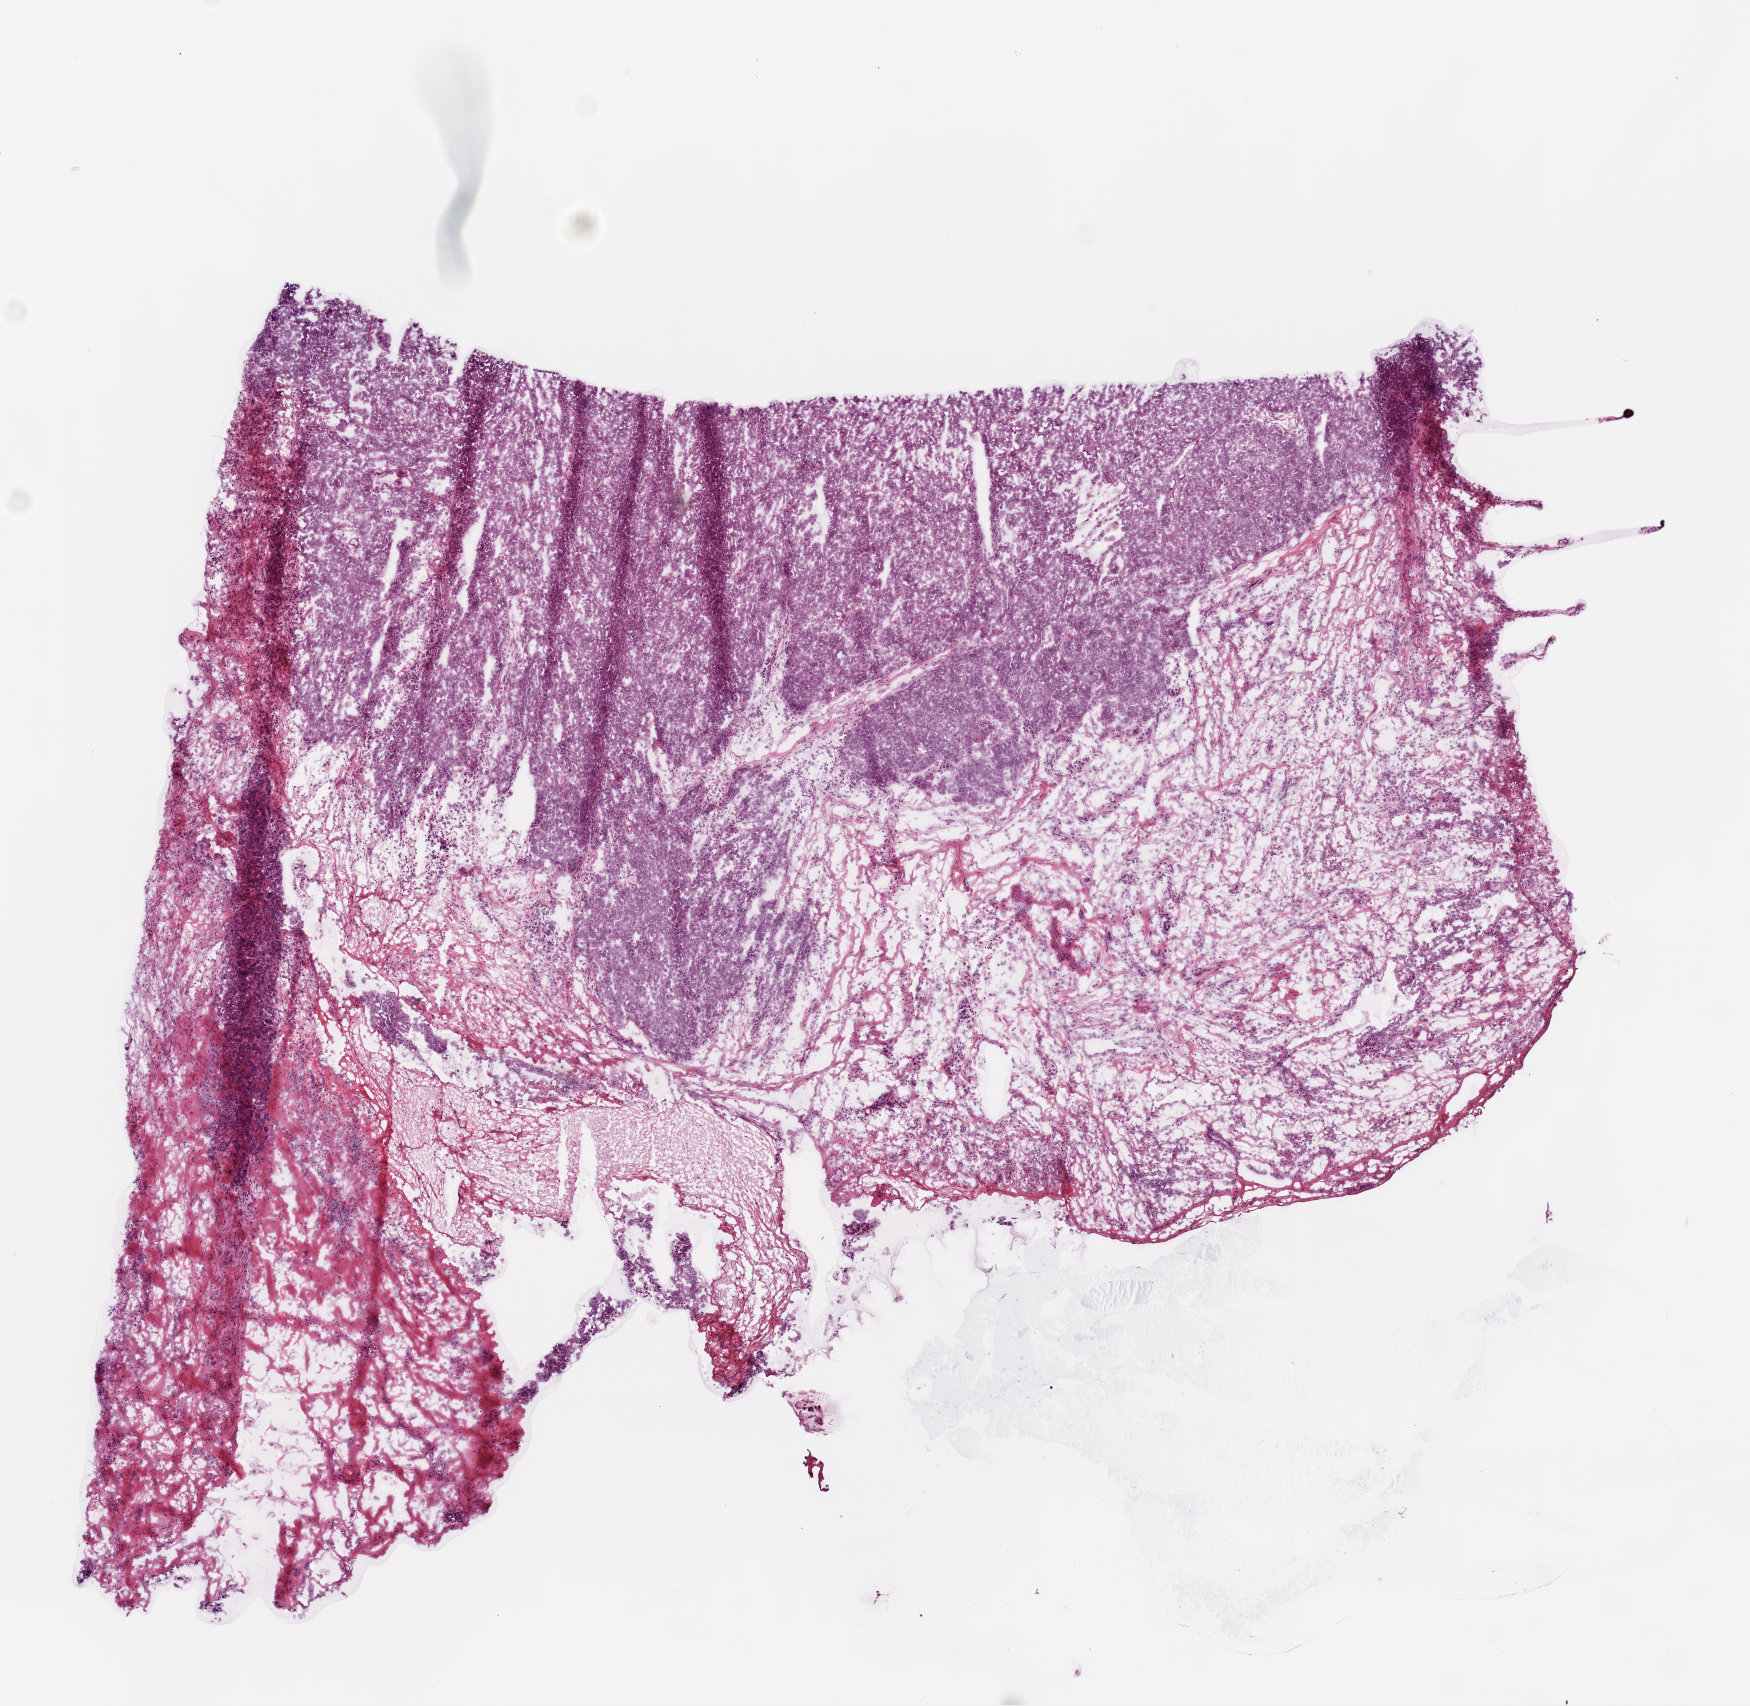
H&E-stained whole-slide image, low-resolution overview of the scanned area, about 7.0 x 6.8 mm (acquisition: 20x scan); frozen section from the bottom of the tissue portion; primary tumour sample from the ovary. Patient: female, age at initial diagnosis 65 years. Histologic grade: G3 (poorly differentiated). Composition of this section per pathologist review: tumour cells 70%, tumour nuclei 70%, normal cells 0%, stromal cells 20%, necrosis 10%. Infiltration values recorded for this section: lymphocyte infiltration 0%, monocyte infiltration 0%, neutrophil infiltration 5%.
• pathologic diagnosis: Serous cystadenocarcinoma, NOS
• FIGO stage: IIIC